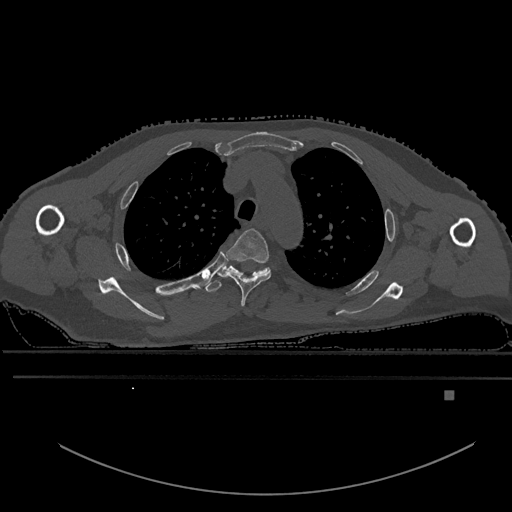
CT including the spine, one axial slice. Slice 438 of 969 in the series (ordered by position). Bone window (W 1800 / L 400 HU). 512 × 512 image matrix, field of view 456 × 456 mm. Male patient, age 82 years. Case-level facts recorded for this patient, not image findings: primary cancer: prostate.
Outlined on this slice (semi-automatic segmentation, software-assisted and operator-edited):
- T3 vertebra: bounding box (x1, y1, x2, y2) in pixels: (220, 228, 271, 307)
- T4 vertebra: (205, 262, 270, 293)